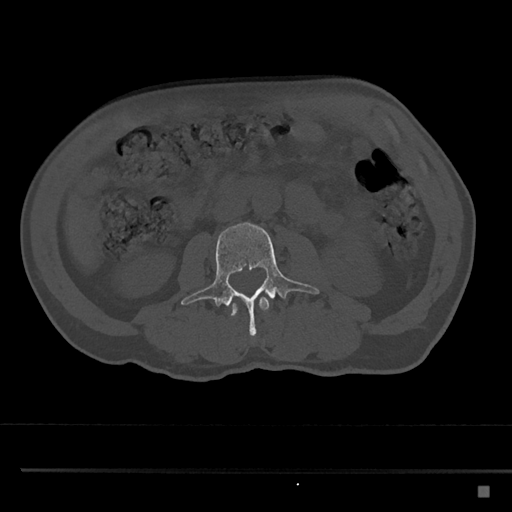
CT including the spine, one axial slice; position 705 of 797 along the scan axis; bone window (W 1800 / L 400 HU); 0.5 mm slice thickness; 512 × 512 image matrix, field of view 391 × 391 mm. Patient: male, 59 years. Case-level facts recorded for this patient, not image findings: primary cancer: prostate.
Structures marked on this image (semi-automatically segmented with operator editing):
- L2 vertebra: box from (x=227, y=297) to (x=270, y=316) px
- L3 vertebra: (x=181, y=222)–(x=320, y=338)